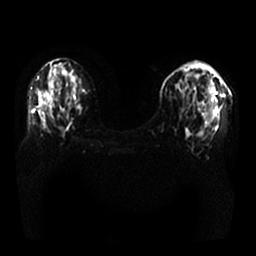
Breast MRI, one axial slice. Position 12 of 25 along the scan axis. Diffusion-weighted series; image 2 of 4 stored at this slice position (different b-values; order by instance number). 1.5 T. 4 mm slice thickness. 256 × 256 image matrix, field of view 350 × 350 mm. Female patient.
Structures marked on this image (manually delineated by an expert):
- tumour on diffusion-weighted imaging: bounding box [x1, y1, x2, y2] px = [208, 87, 213, 93]